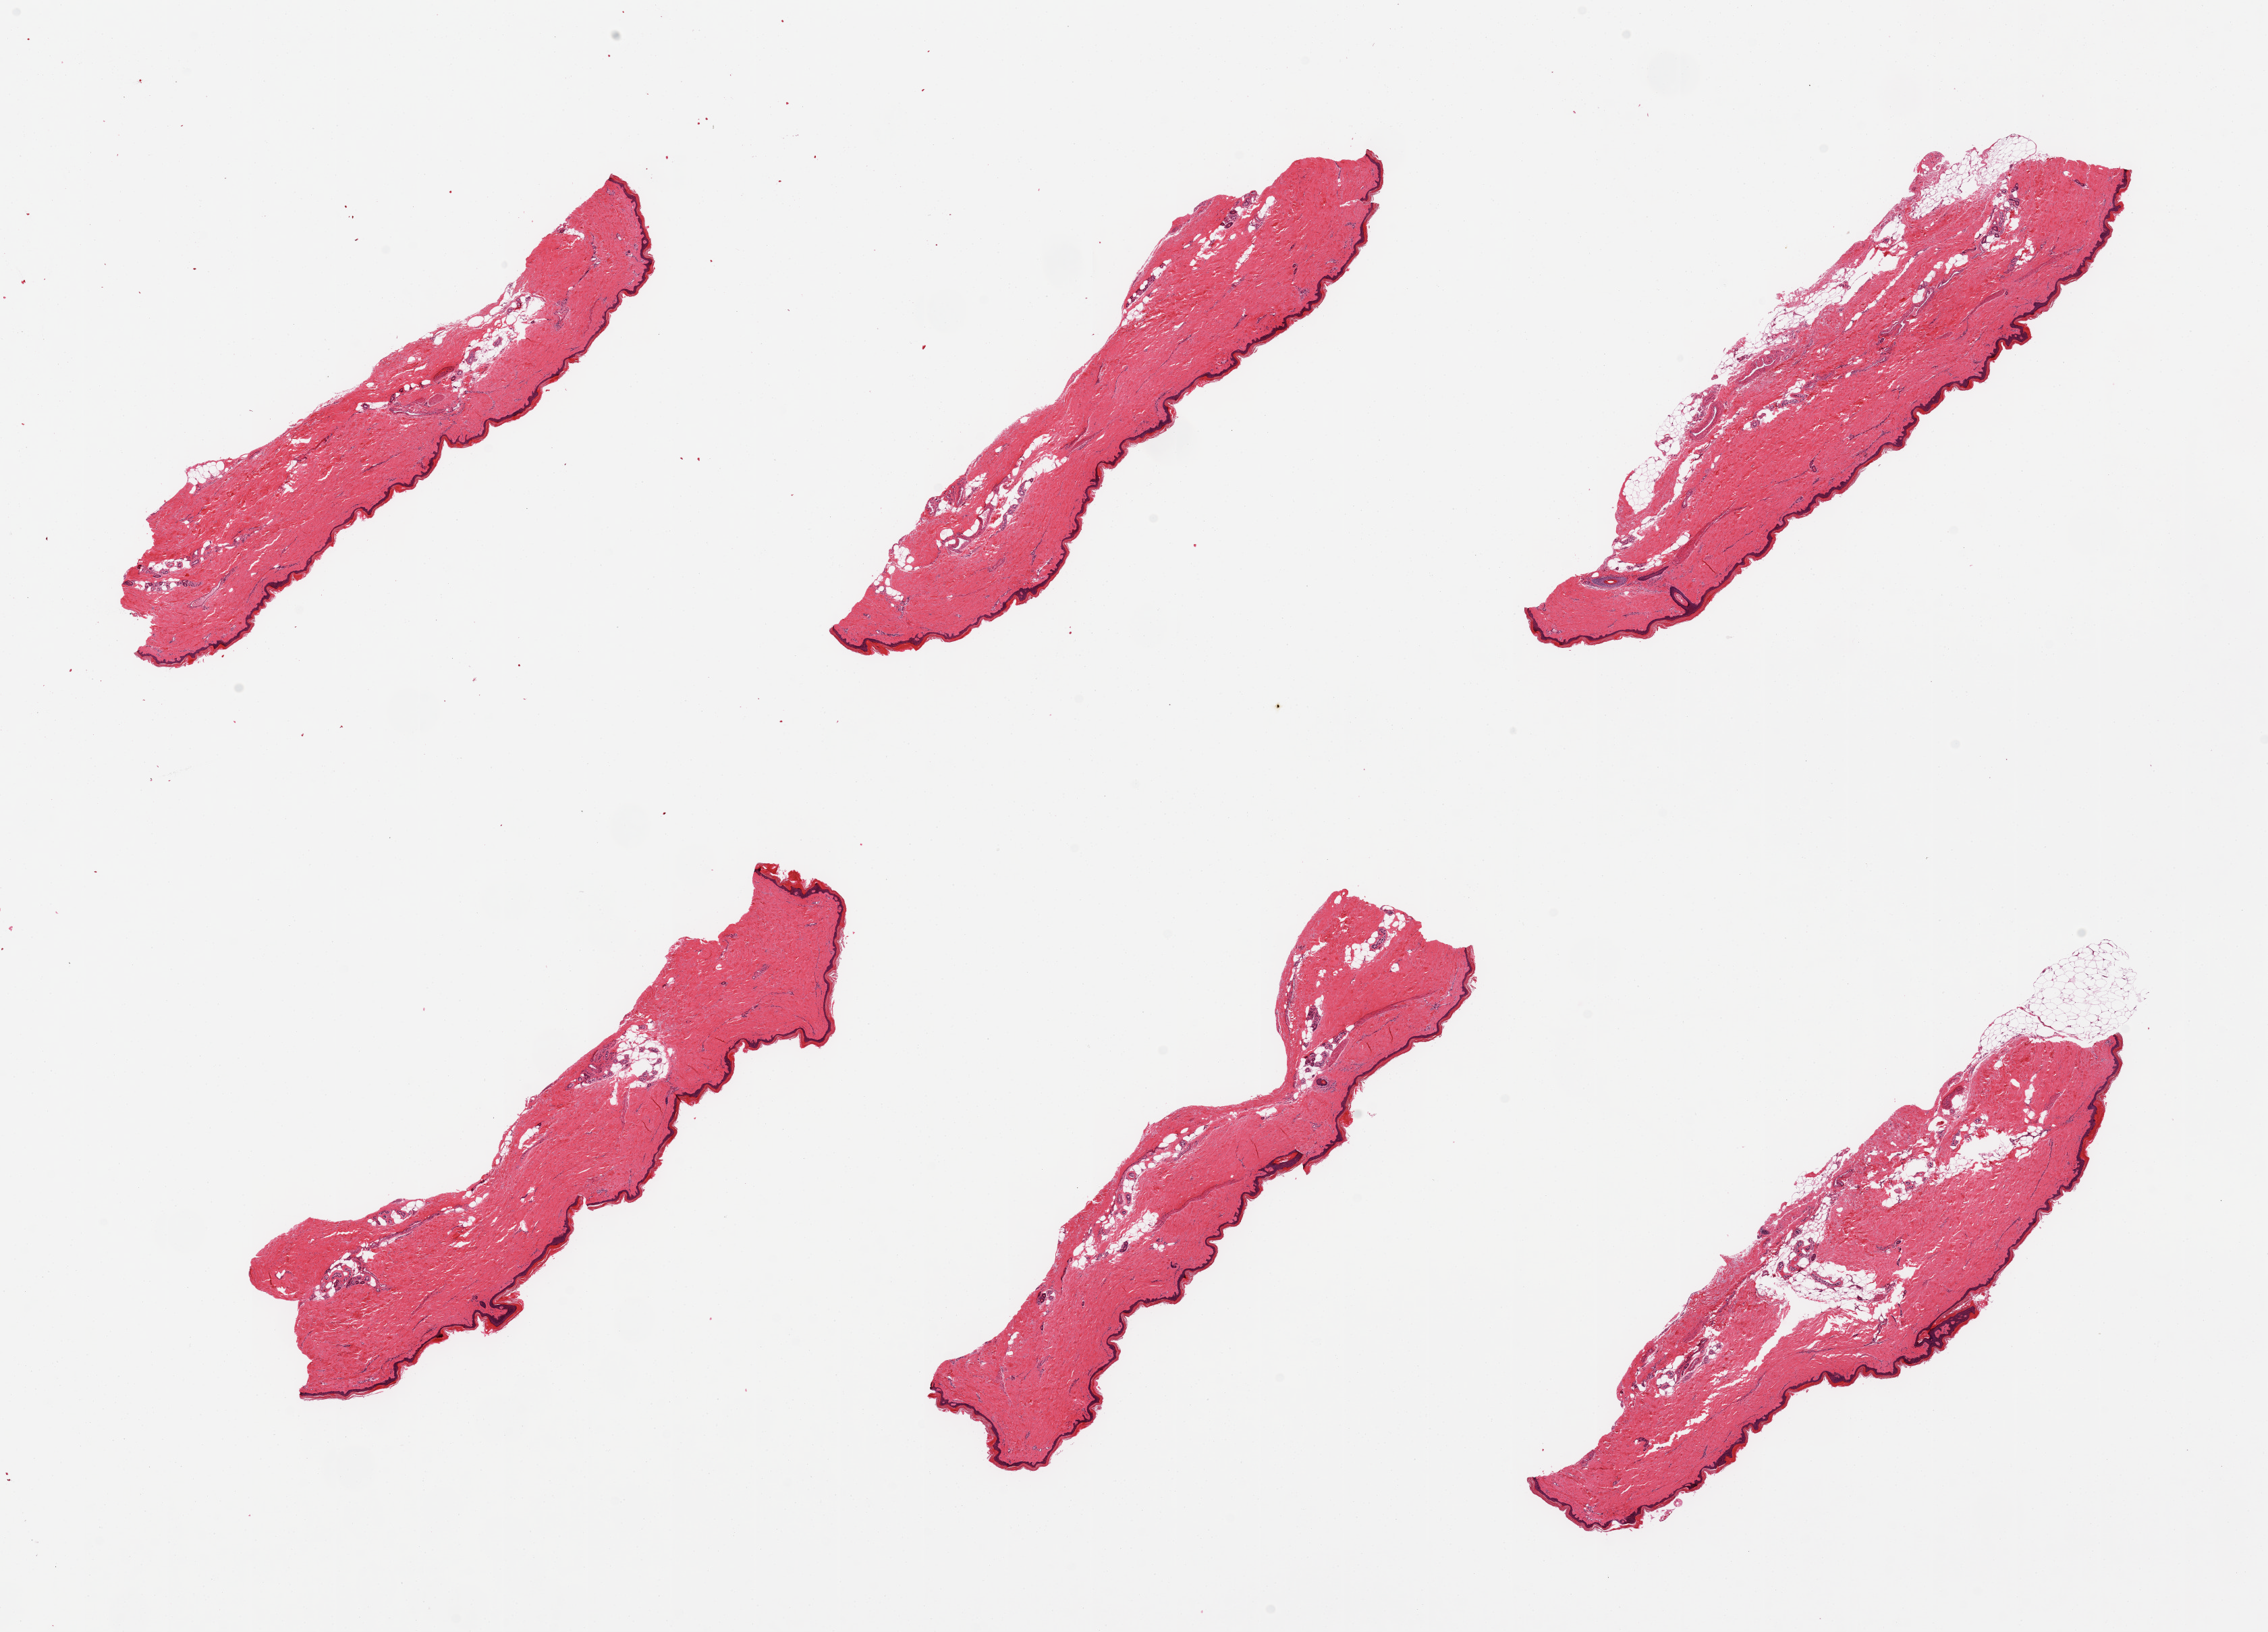
Haematoxylin and eosin whole-slide image — whole scanned area (about 26.6 x 19.1 mm, acquisition: 20x scan) shown as a low-resolution overview, PAXgene-fixed, paraffin-embedded tissue, section of skin of lower leg (target tissue), donor tissue sample.
- review note (as recorded): 6 pieces, no dermal fat; squamous epithelium is ~50 microns